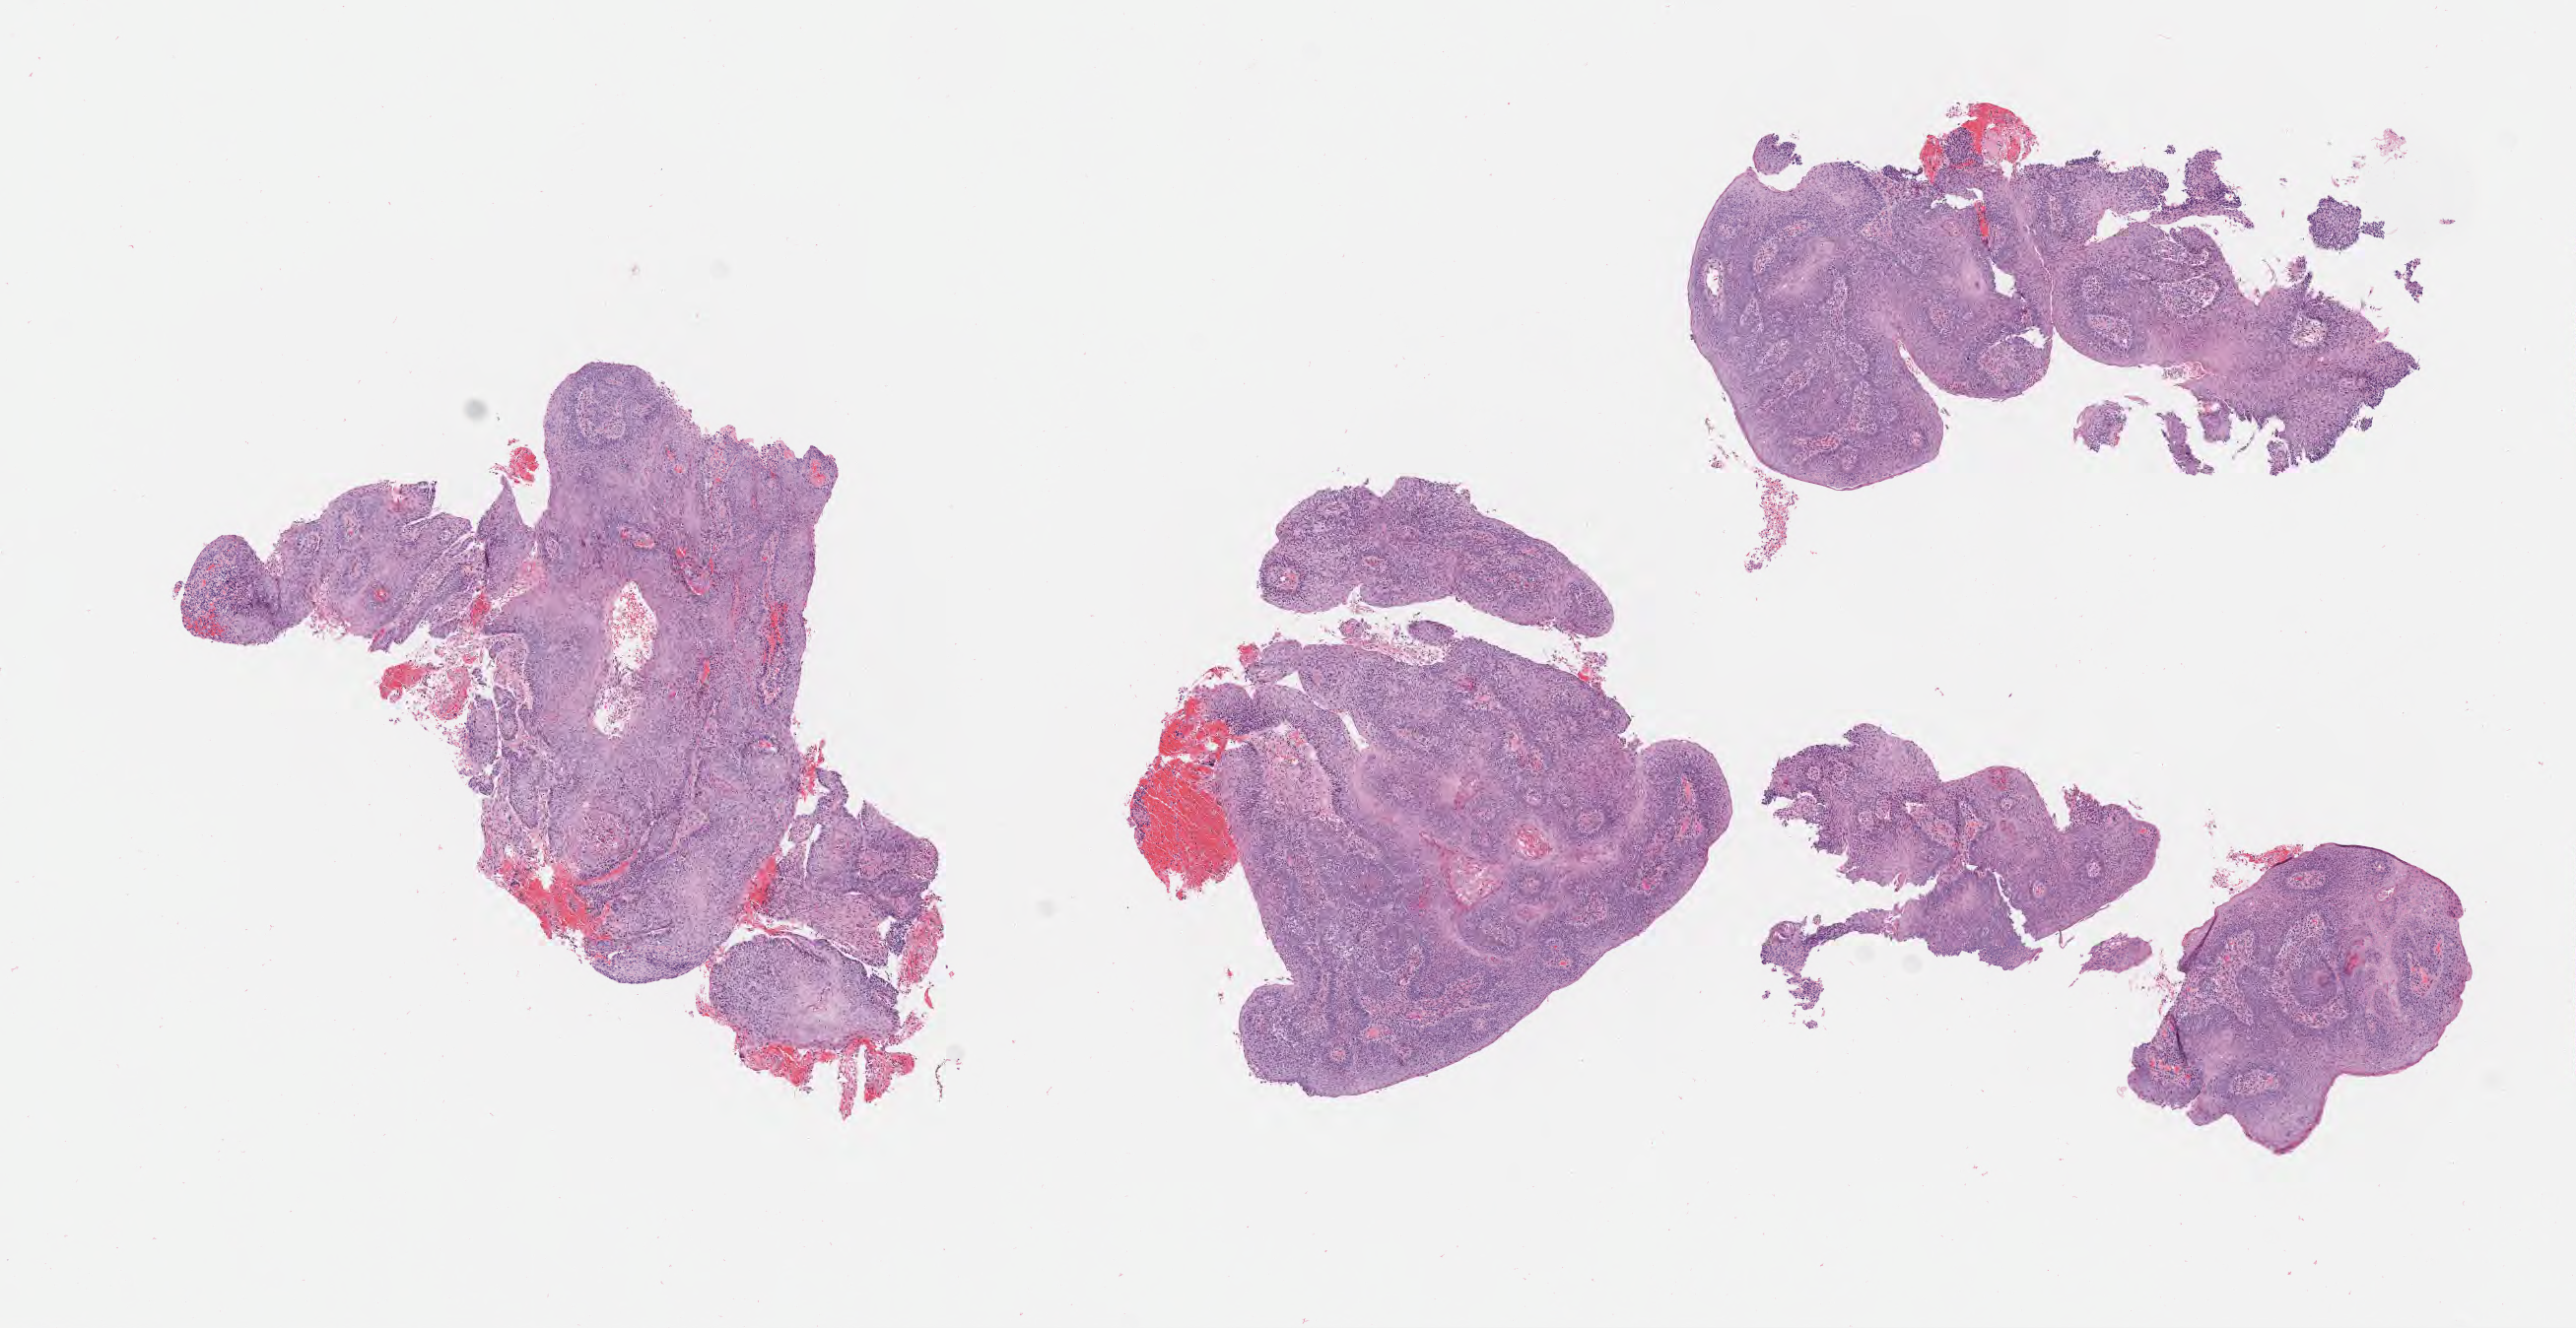
Digitized hematoxylin and eosin (H&E)-stained section, shown as a low-resolution overview of the whole scanned area (about 10.6 x 5.5 mm), specimen: tumor tissue, anatomic site: cervix. Patient: female, 48 years old.
• histologic diagnosis: Squamous cell carcinoma, keratinizing, NOS